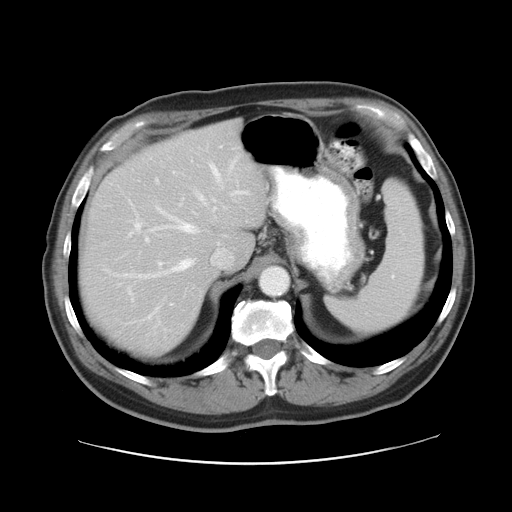
Contrast-enhanced abdominal CT, one axial slice. Position 21 of 28 along the scan axis. Intravenous contrast given. Soft-tissue window (W 400 / L 40 HU). 7.5 mm slice thickness. 512 × 512 image matrix, field of view 402 × 402 mm. Male patient, age 74 years. From the clinical record (not read from this slice): diagnosis: colorectal cancer liver metastases, imaged before liver resection; multiple liver metastases: no; largest metastasis: 5 cm; disease in both lobes: no.
Annotated regions visible in this slice (outlined manually by an expert reader):
- hepatic veins: bounding box [x1, y1, x2, y2] px = [124, 163, 223, 278]
- liver: [83, 125, 265, 351]
- planned liver remnant (the part of the liver to remain after resection): [83, 176, 215, 351]
- portal vein (with intrahepatic branches): [237, 191, 245, 194]